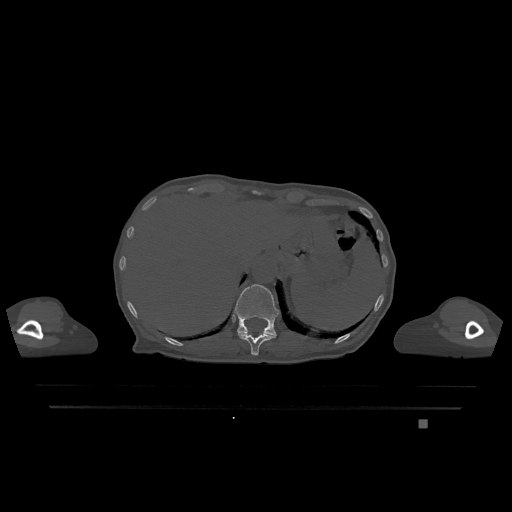
CT including the spine, one axial slice; slice 559 of 1317 in the series (ordered by position); bone window (W 1800 / L 400 HU); 0.5 mm slice thickness; 512 × 512 image matrix. Female patient, age 74 years. From the clinical record (not read from this slice): primary cancer: lung; vertebrae with lytic lesions (as recorded): T1, T4, T5, T6, L4, L5.
Annotated regions visible in this slice (semi-automatically segmented with operator editing):
- T11 vertebra: box from (x=238, y=334) to (x=276, y=355) px
- T12 vertebra: (x=234, y=284)–(x=279, y=336)